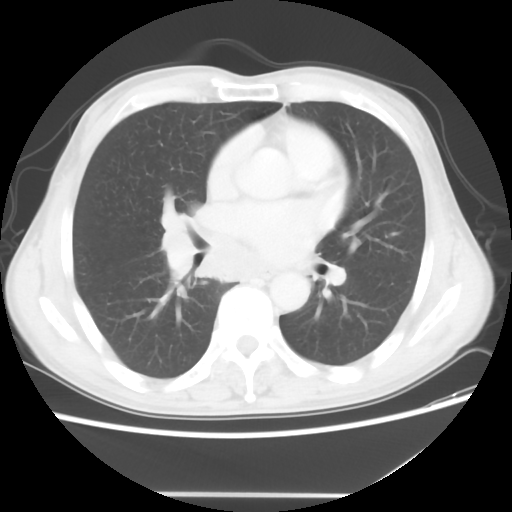
Chest CT, one axial slice; slice 27 of 56 in the series (ordered by position); reconstruction kernel STANDARD; 120 kVp; lung window (W 1500 / L -600 HU); 5 mm slice thickness; 512 × 512 image matrix, field of view 344 × 344 mm. Patient: male, 65 years. From the clinical record (not read from this slice): clinical TNM (as recorded): T1c N3 M0; histopathological grade: G3.
Outlined on this slice (rectangle marked by the reading radiologist):
- lung tumour (recorded histology: small cell carcinoma): bounding box <152,201,198,283> (left, top, right, bottom; pixels)